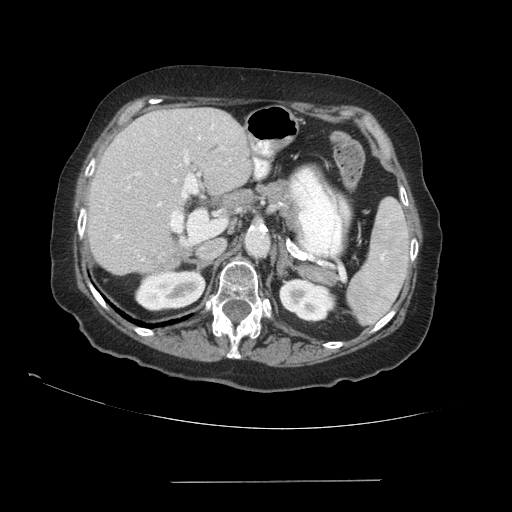
Contrast-enhanced abdominal CT (liver protocol), one axial slice; position 57 of 89 along the scan axis; reconstruction kernel STANDARD; 140 kVp; soft-tissue window (W 400 / L 40 HU); 2.5 mm slice thickness; 512 × 512 image matrix. Case-level facts recorded for this patient, not image findings: diagnosis: hepatocellular carcinoma (patient treated with transarterial chemoembolisation; whether this scan precedes or follows treatment is not stated here); TNM stage (as recorded): Stage-IVA; Child-Pugh class: A; tumour differentiation: poorly differentiated; tumour nodularity: uninodular.
Annotated regions visible in this slice (semi-automatically segmented with operator editing):
- liver parenchyma outside the tumour (the mass and vessels are separate outlines, so this box may not span the whole liver): bounding box (x1, y1, x2, y2) in pixels: (88, 108, 252, 274)
- liver vessels: (115, 124, 215, 260)